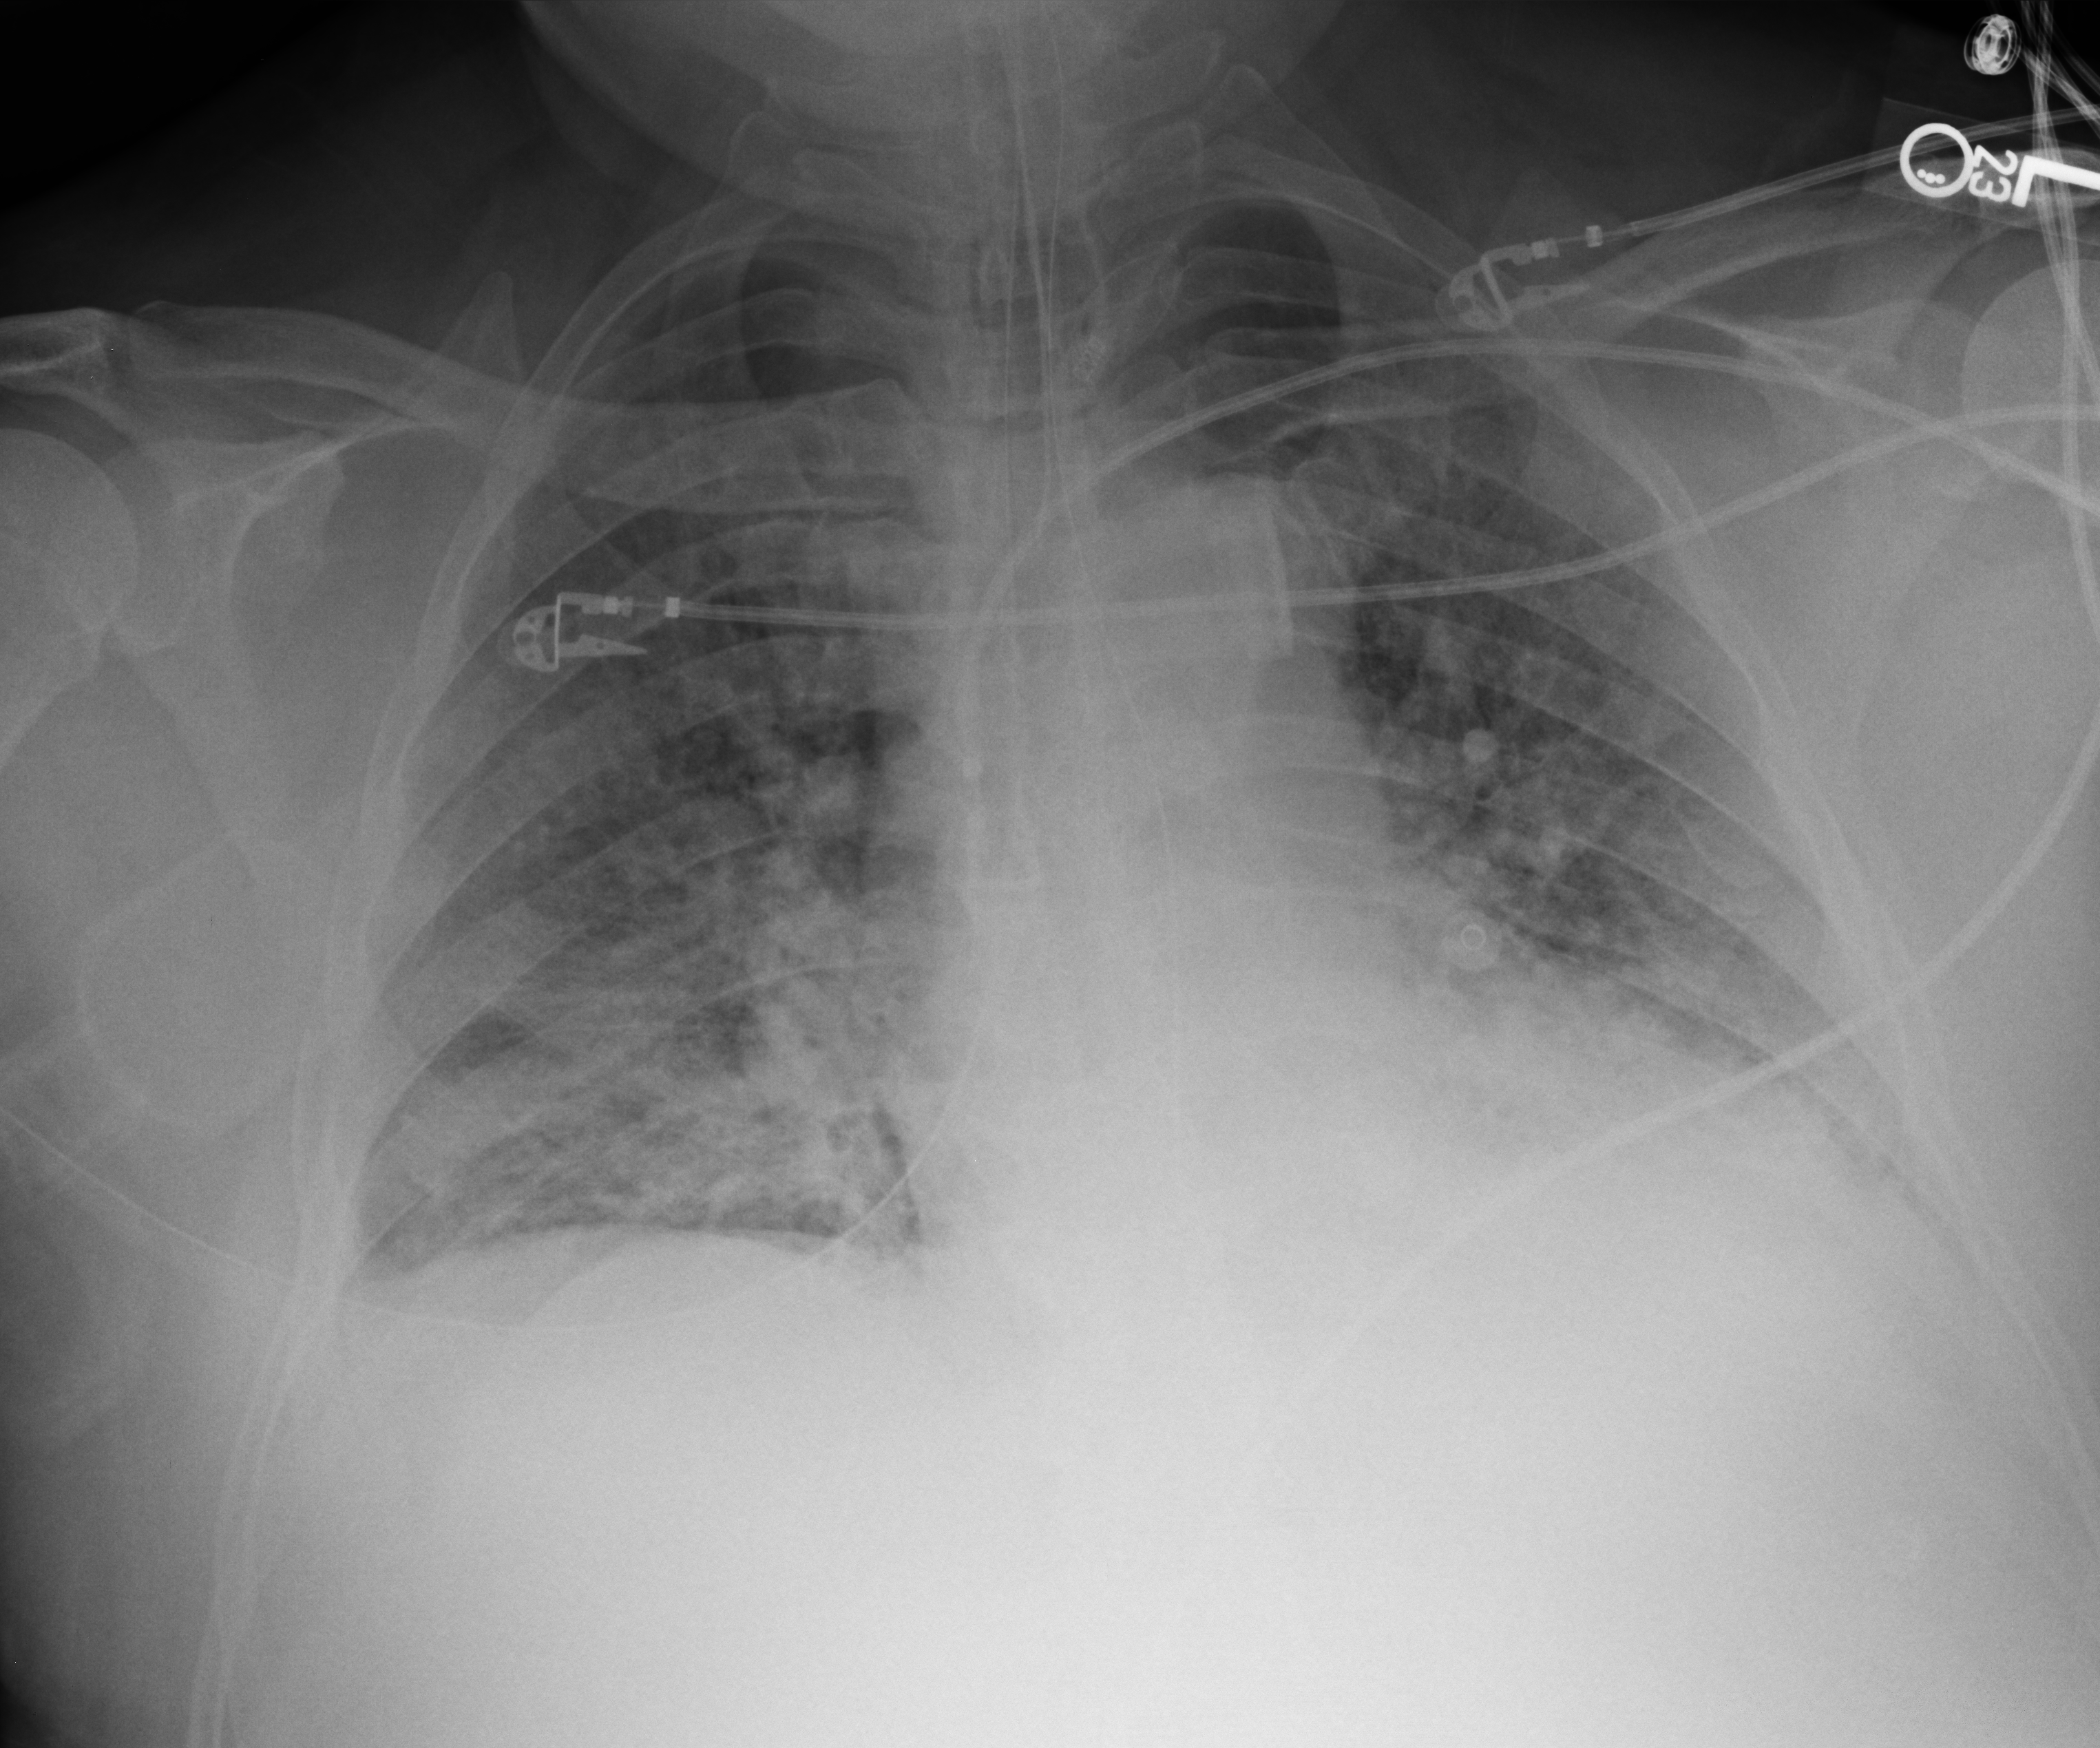
Portable chest radiograph; anteroposterior (AP) projection. Male patient hospitalised with COVID-19, age 60–74 years.
Hospital-stay facts (about this admission, not read from this image; timing relative to this image not recorded):
- length of hospital stay: 28 days
- admitted to intensive care during this hospital stay: yes